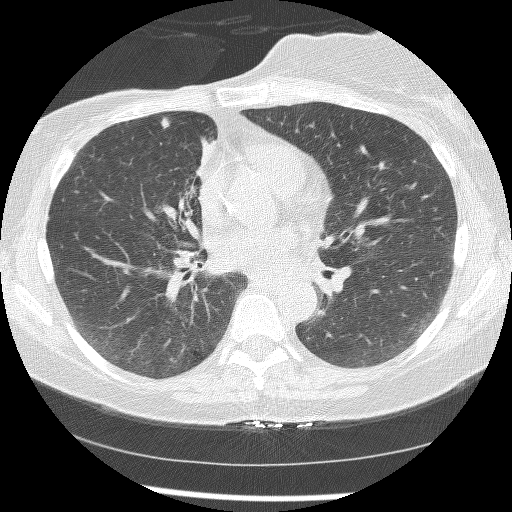
Low-dose screening chest CT, axial slice; baseline screening round; lung window (W 1500 / L -600 HU); 2.5 mm slice thickness; lung (sharp) reconstruction kernel (BONE); 120 kVp; slice 77 of 172 in the series. Female, age 56 years at enrolment. Current smoker at enrolment.
Expert-annotated lung lesion, bounding box <149,110,180,141> (left, top, right, bottom; pixels). The screening reader recorded 2 non-calcified nodules or masses ≥4 mm on this exam (right lower lobe, right middle lobe); which of them this box marks is not recorded. Official screen result: positive, change unspecified: nodule(s) >= 4 mm or enlarging nodule(s), mass(es), or other non-specific abnormalities suspicious for lung cancer. Lung cancer was diagnosed 1185 days after this screen: adenocarcinoma, NOS, right upper lobe, stage IIIB (AJCC 6th edition), 8 mm at pathology.